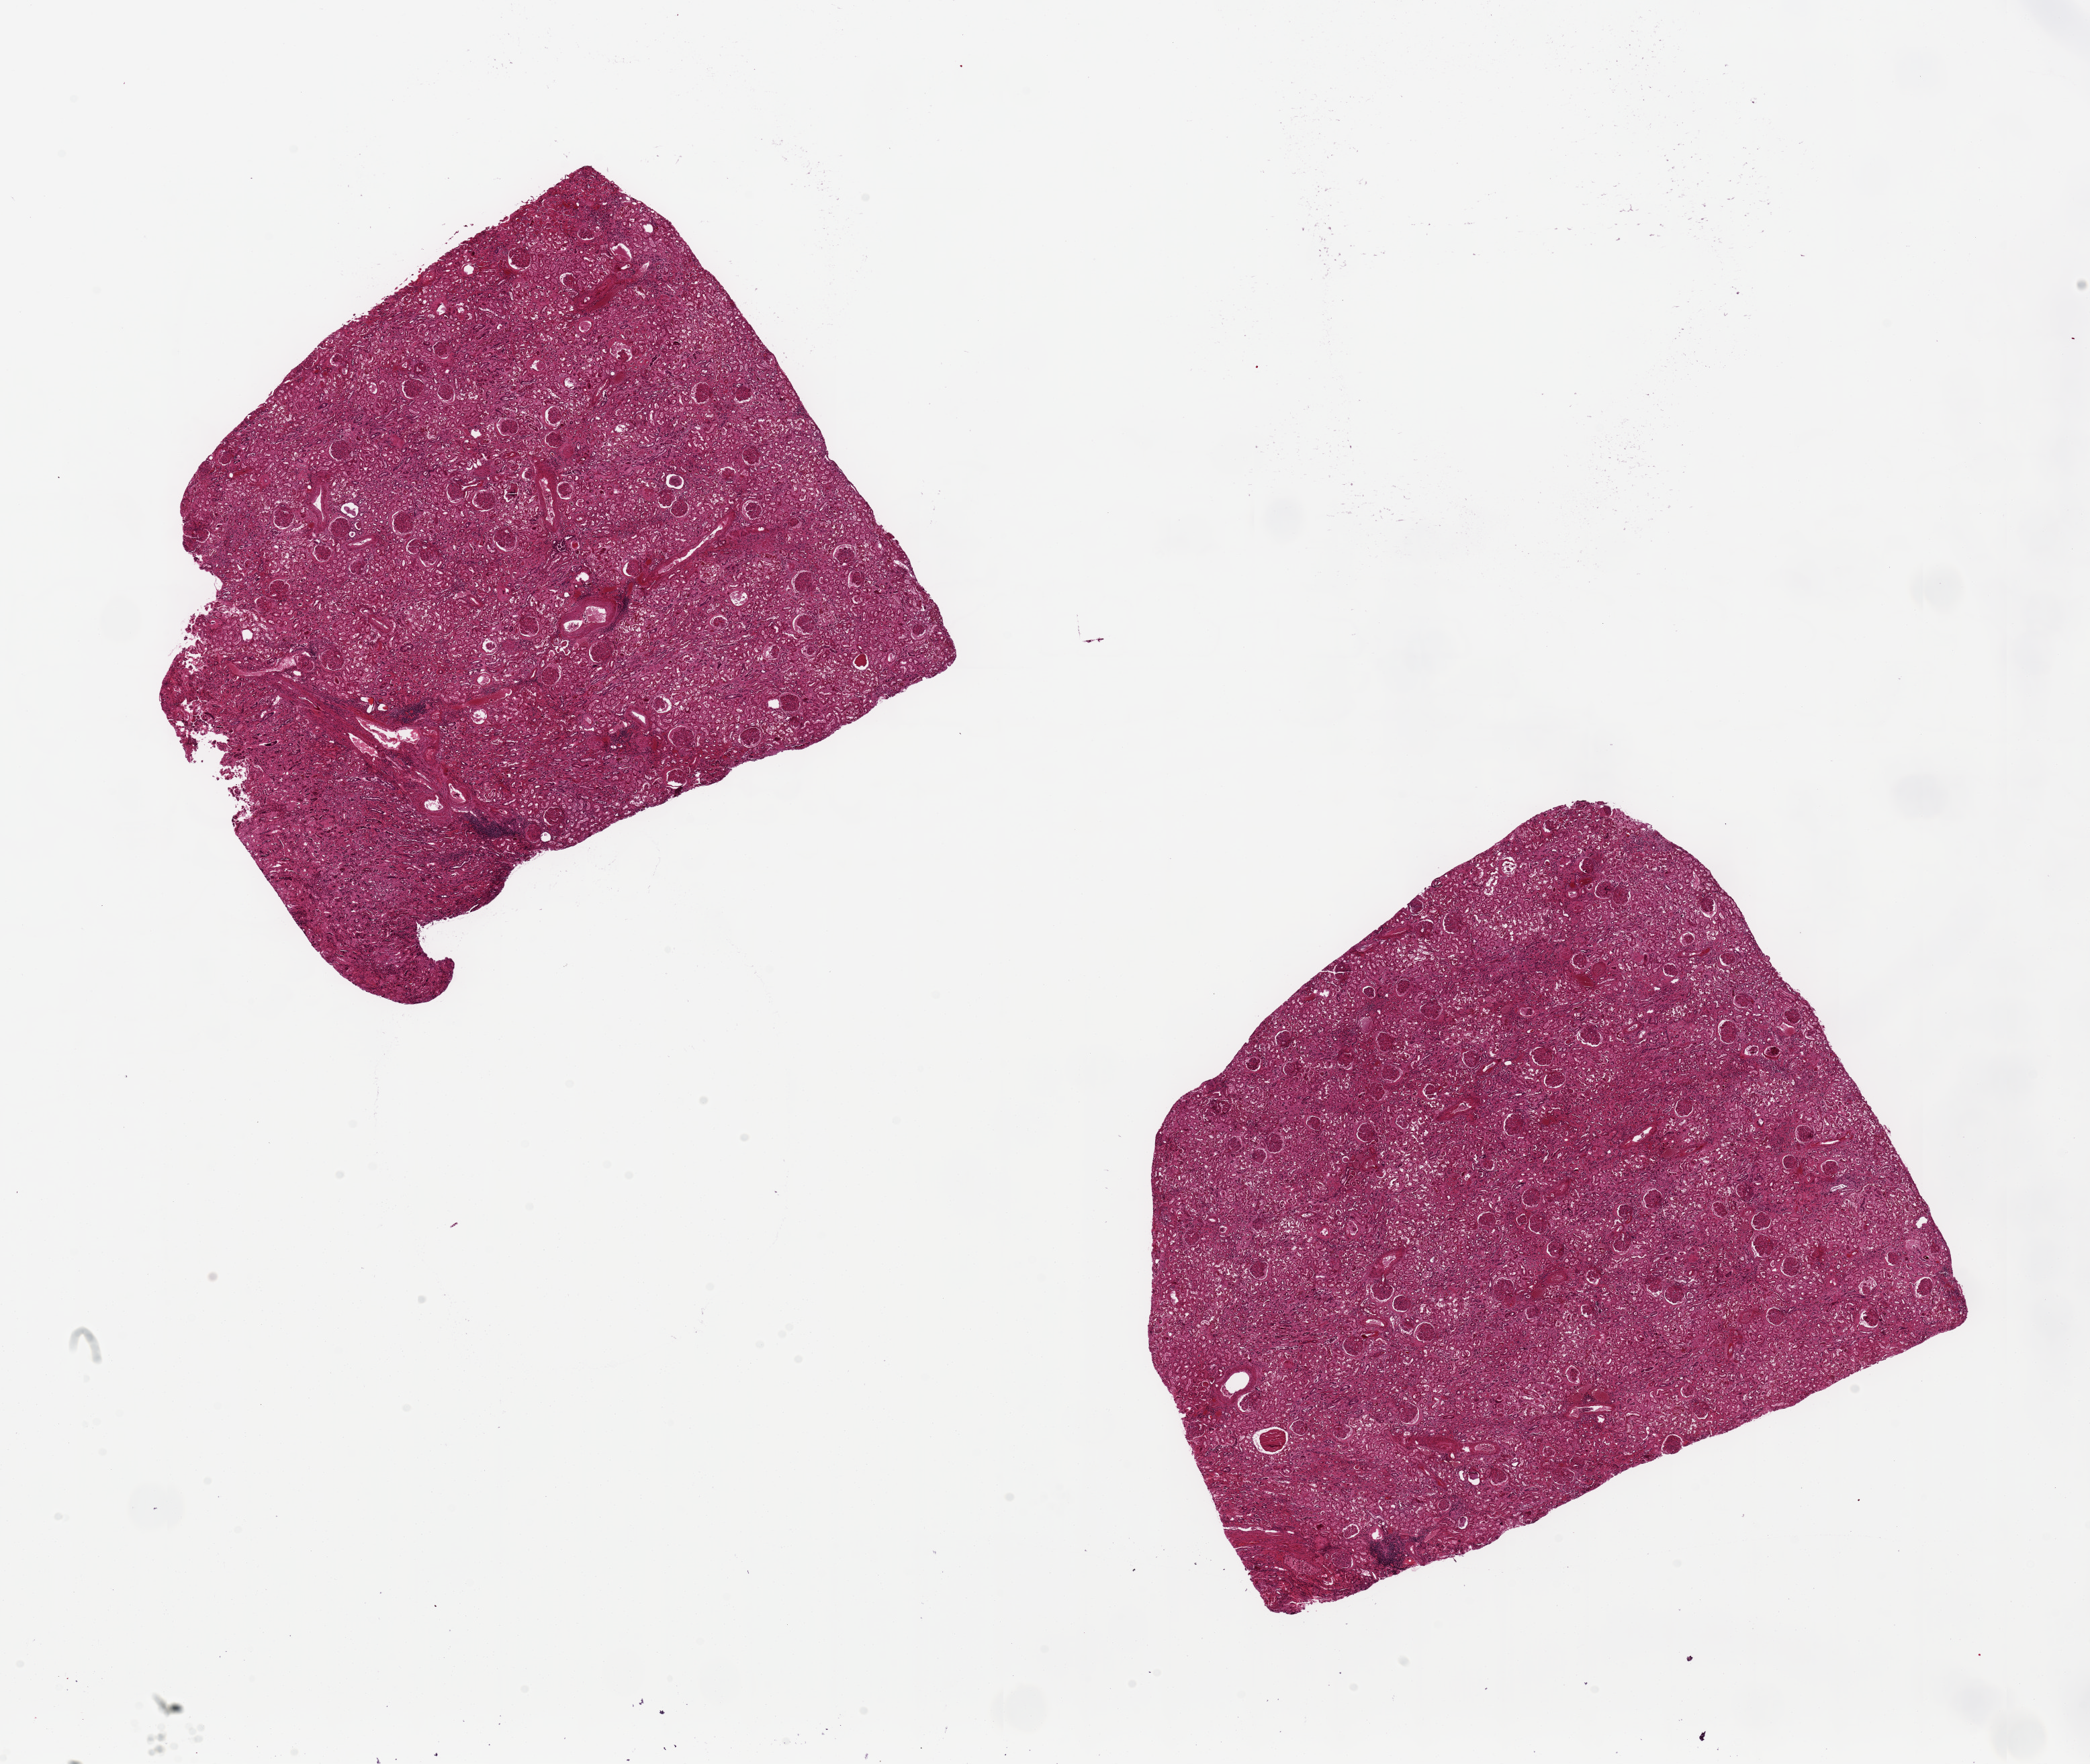
Whole-slide image, hematoxylin and eosin (H&E) stain, brightfield — low-resolution overview of the scanned area, about 24.6 x 20.8 mm (slide scanned at 20x), PAXgene-fixed paraffin-embedded (PFPE) section, sampled site (target tissue): renal cortex, tissue donor sample.
• reviewer comment on this tissue sample: 2 ~8x7mm pieces, both with glomurli. Tubules badly autolyzed